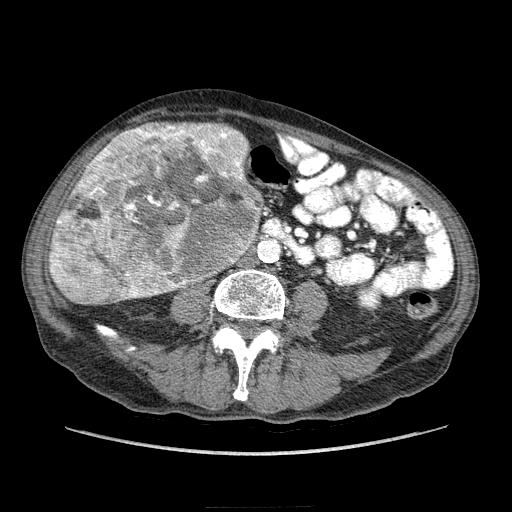
Contrast-enhanced abdominal CT (liver protocol), one axial slice. Position 55 of 218 along the scan axis. Reconstruction kernel STANDARD. Soft-tissue window (W 400 / L 40 HU). 2.5 mm slice thickness. 512 × 512 image matrix. Case-level facts recorded for this patient, not image findings: diagnosis: hepatocellular carcinoma (patient treated with transarterial chemoembolisation; whether this scan precedes or follows treatment is not stated here); TNM stage (as recorded): Stage-IIIA; Child-Pugh class: A; tumour differentiation: well differentiated; tumour nodularity: multinodular.
Outlined on this slice (semi-automatically segmented with operator editing):
- liver parenchyma outside the tumour (the mass and vessels are separate outlines, so this box may not span the whole liver): bounding box <49,124,260,302> (left, top, right, bottom; pixels)
- mass: <49,120,259,306>